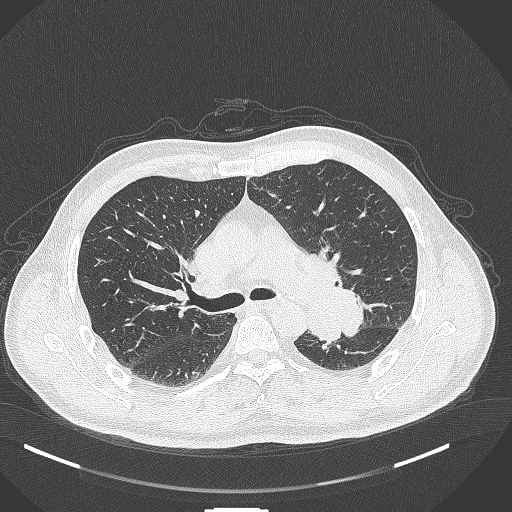
Chest CT, one axial slice; reconstruction kernel B70f; lung window (W 1500 / L -600 HU); 1 mm slice thickness; 512 × 512 image matrix, field of view 400 × 400 mm. Patient: male, 55 years. Case-level facts recorded for this patient, not image findings: clinical TNM (as recorded): T3 N0 M1c.
Structures marked on this image (rectangle marked by the reading radiologist):
- lung tumour (recorded histology: adenocarcinoma): box from (x=300, y=292) to (x=346, y=350) px